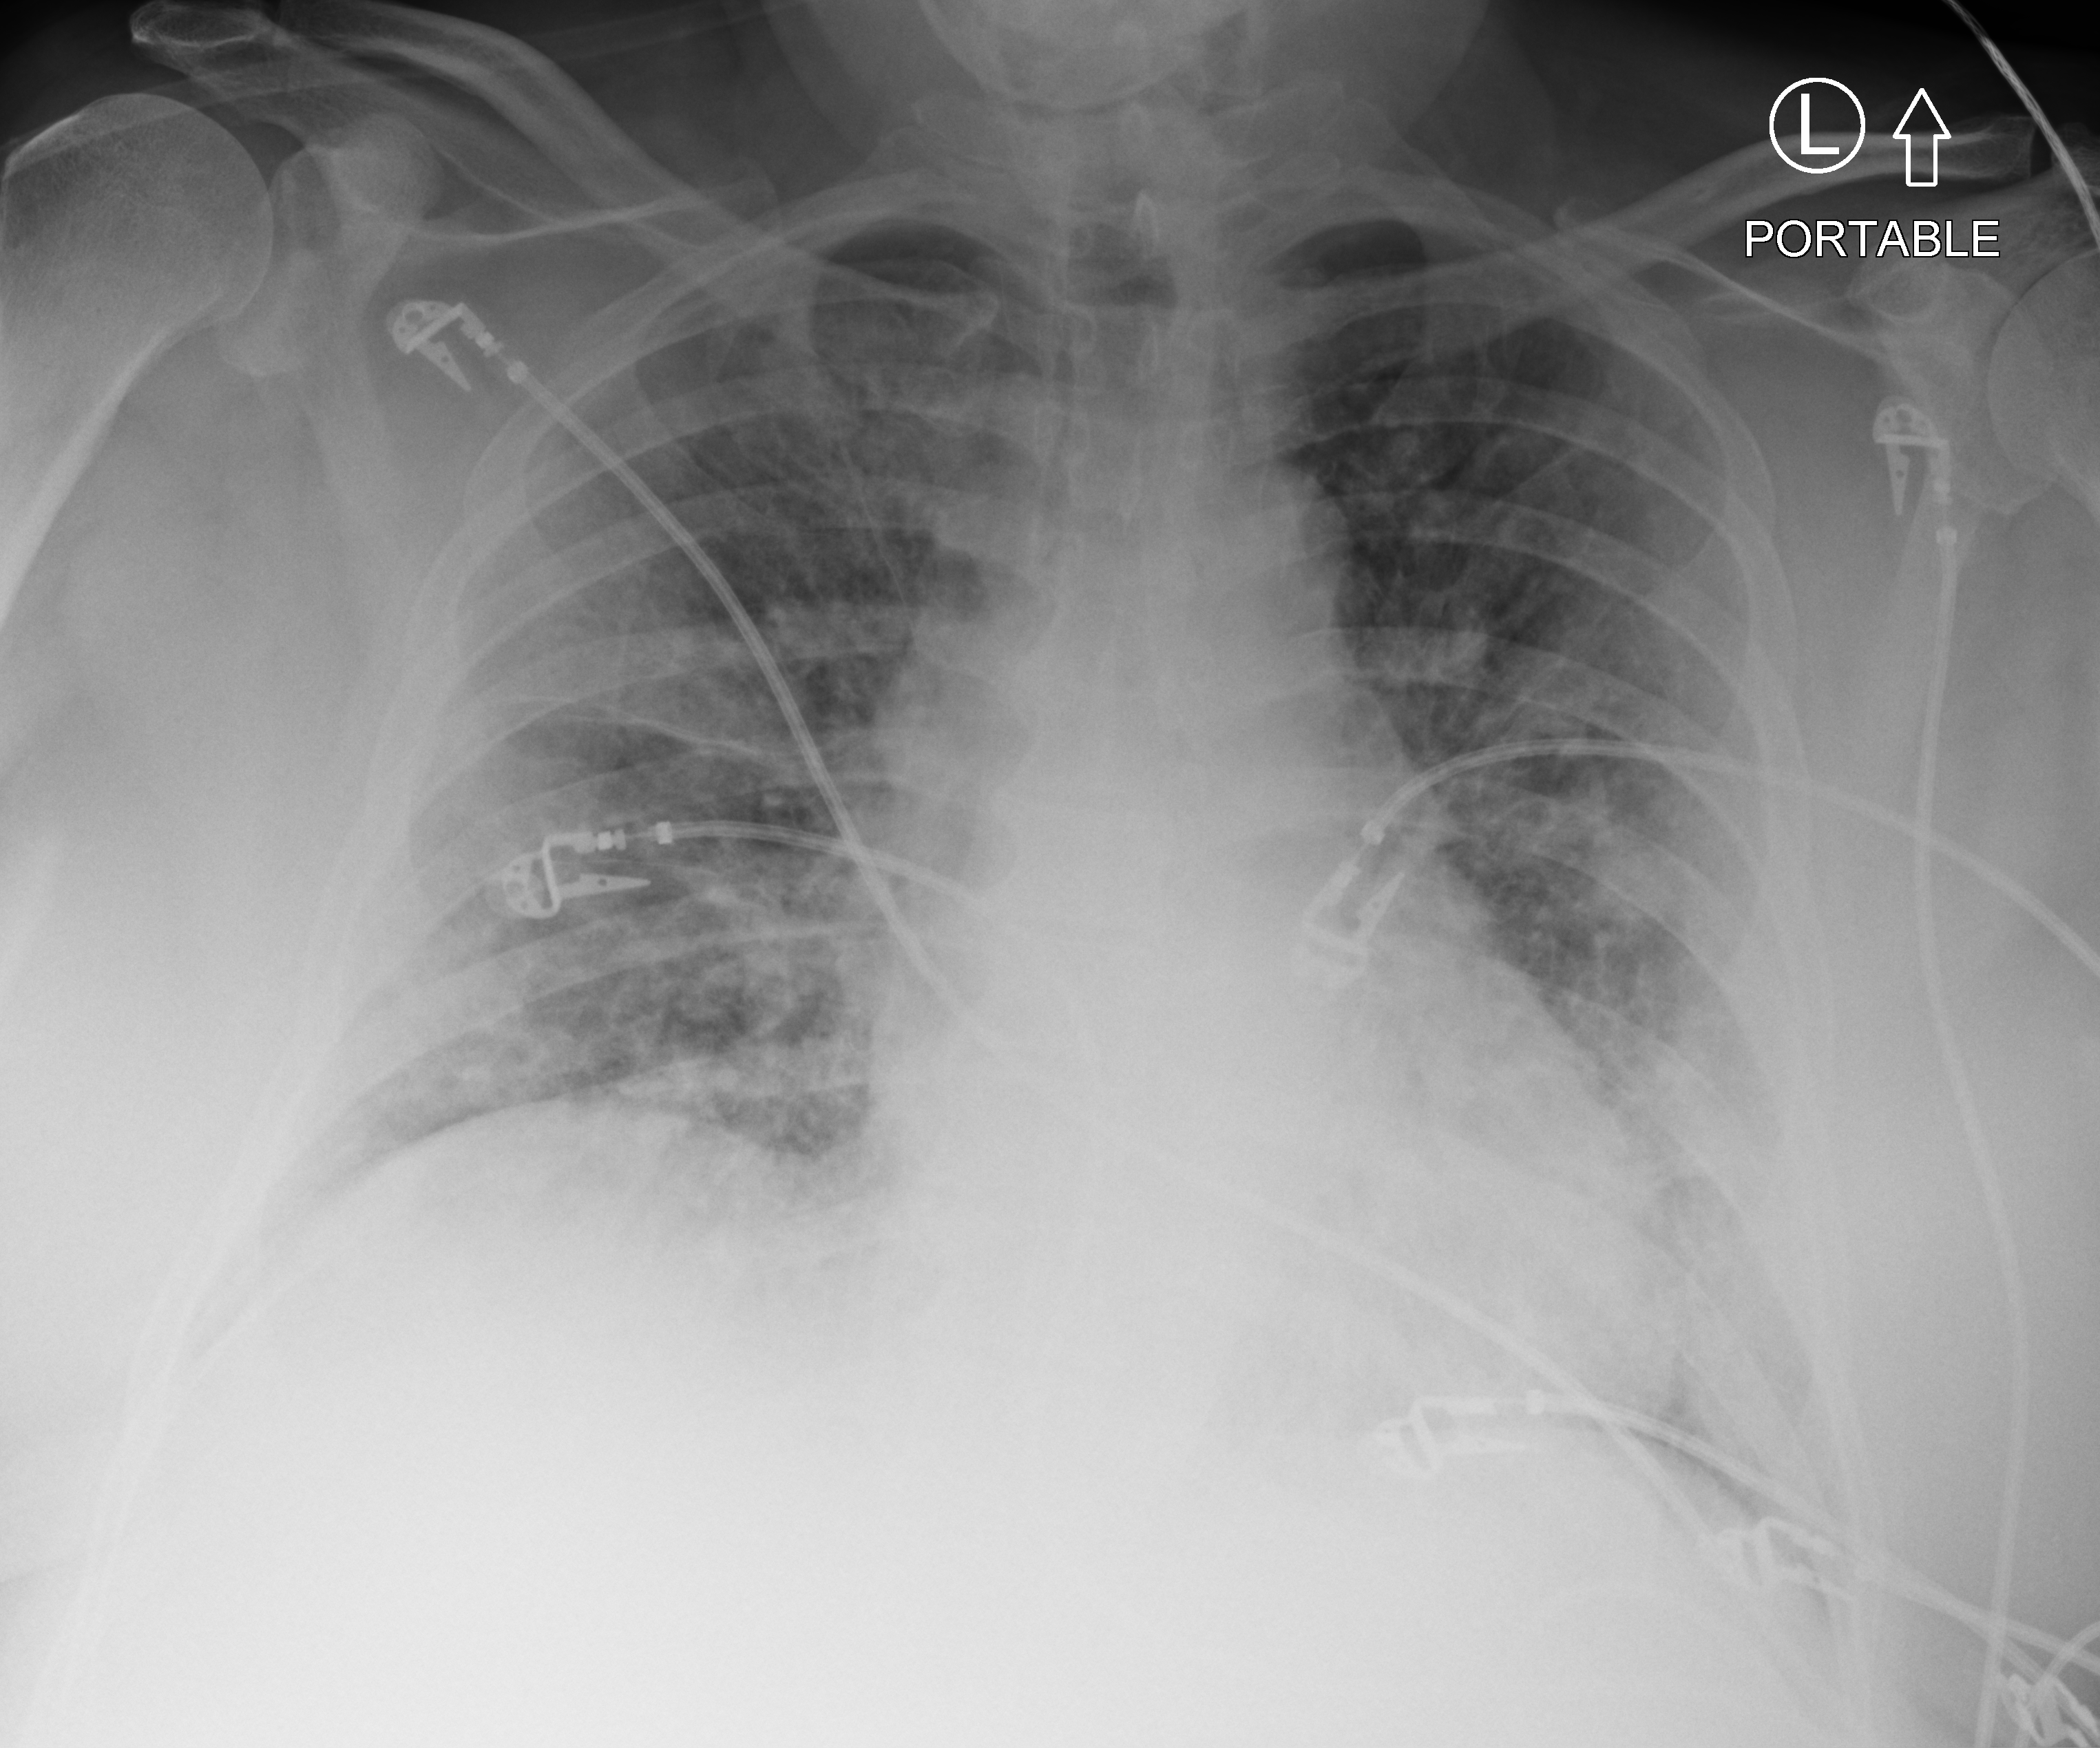
Portable chest radiograph, anteroposterior (AP) projection. Patient hospitalised with COVID-19; male, aged 60–74 years.
From the hospital-stay record, not from the radiograph (when in the stay this image was taken is not recorded):
- mechanically ventilated during this hospital stay: yes